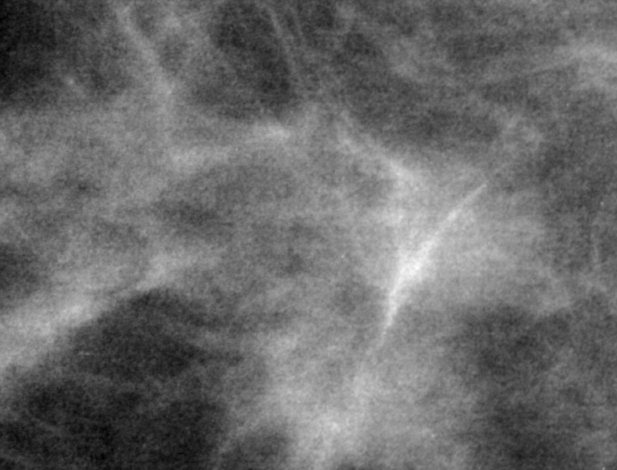
Cropped region of a digitized screen-film mammogram centred on a radiologist-marked abnormality, left breast, CC view, BI-RADS breast density category 2 (scale 1–4).
- Mass, shape irregular, margins ill defined; BI-RADS assessment category 4; pathology result (as recorded, not read from the image): malignant.